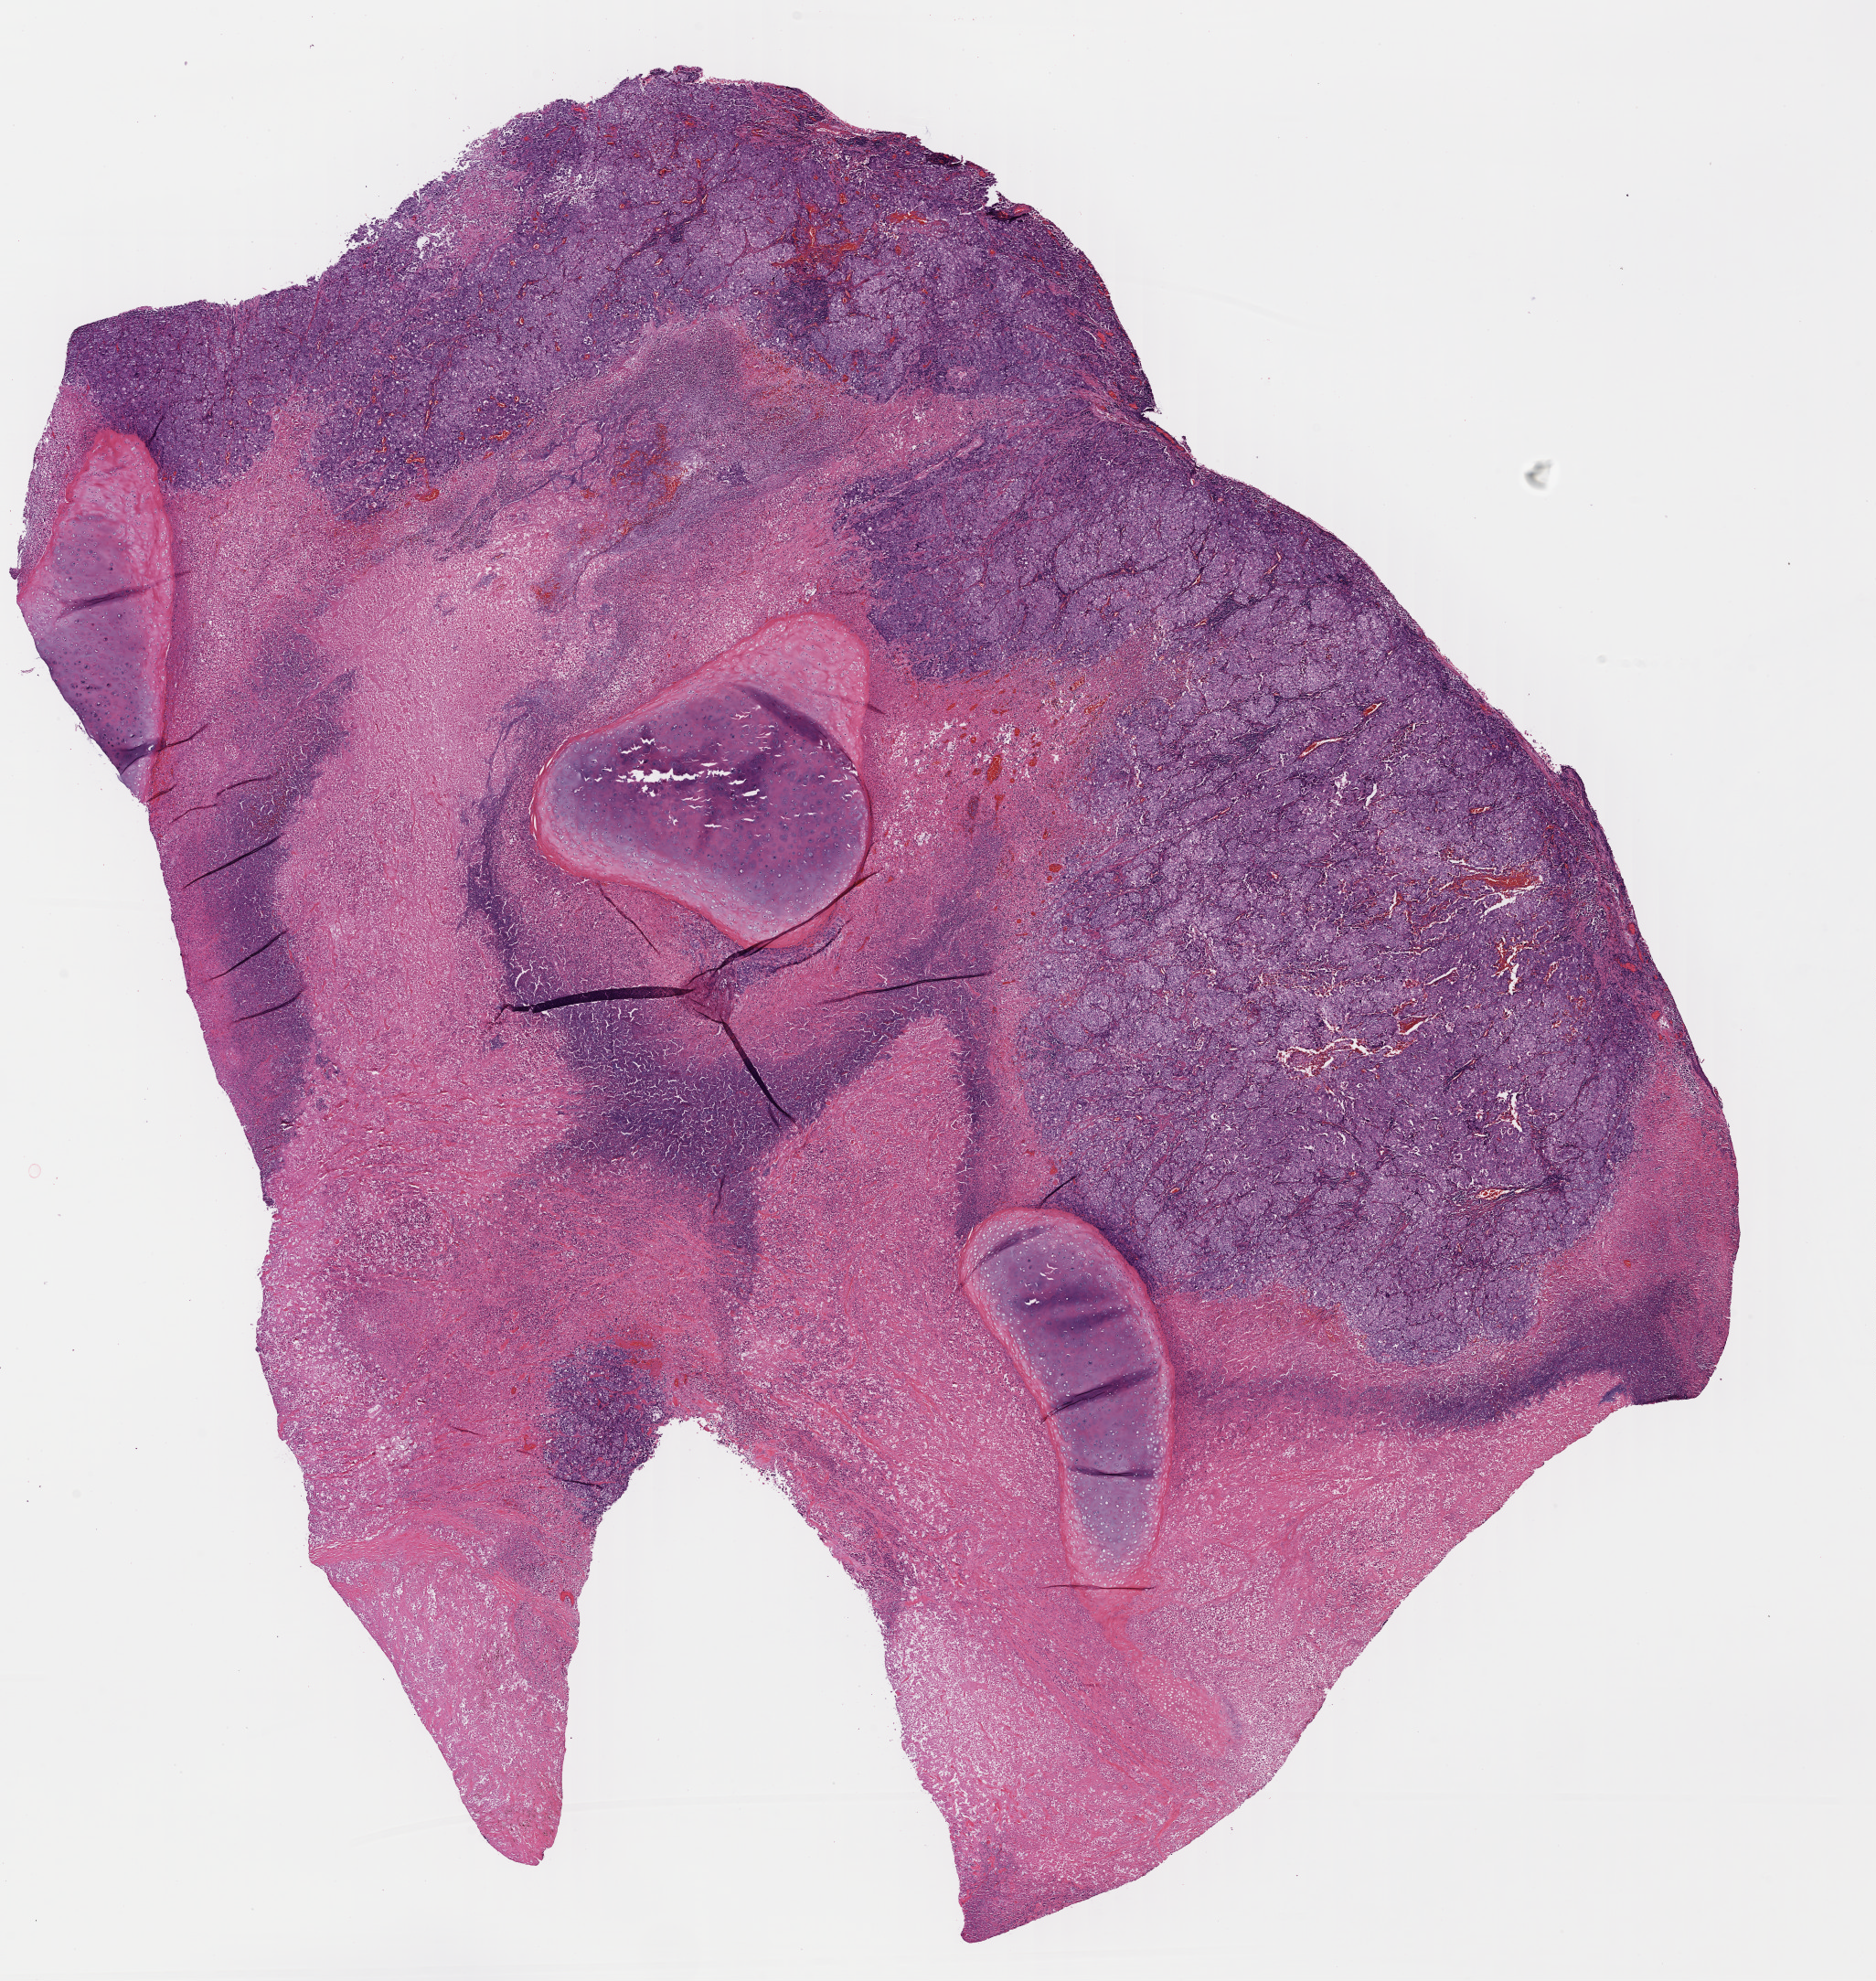
H&E whole-slide image, whole scanned area (about 16.1 x 17.0 mm) shown as a low-resolution overview; formalin-fixed paraffin-embedded (FFPE) diagnostic section; sample: primary tumour, lung. Patient: female, age at initial diagnosis 40 years.
• AJCC pathologic stage: IV (7th edition)
• laterality: right
• TNM: T3 N2 M1b
• histologic diagnosis: Adenocarcinoma, NOS (upper lobe, lung)